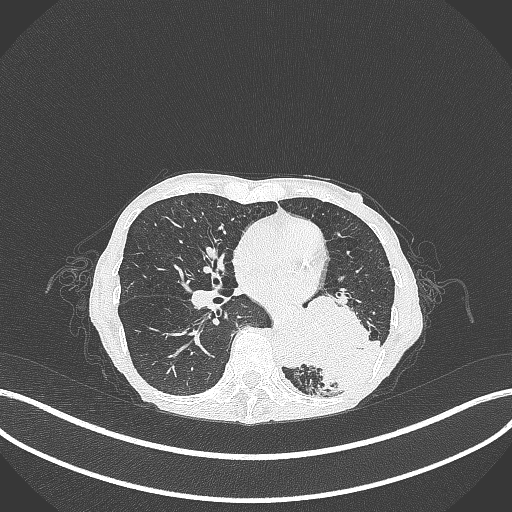
Chest CT, one axial slice. Slice 125 of 347 in the series (ordered by position). Reconstruction kernel B70f. Lung window (W 1500 / L -600 HU). 512 × 512 image matrix, field of view 400 × 400 mm. Female patient, age 70 years. Case-level facts recorded for this patient, not image findings: clinical TNM (as recorded): T3 N0 M0; histopathological grade: G3.
Structures marked on this image (rectangle marked by the reading radiologist):
- lung tumour (recorded histology: small cell carcinoma): bounding box [x1, y1, x2, y2] px = [301, 295, 385, 398]